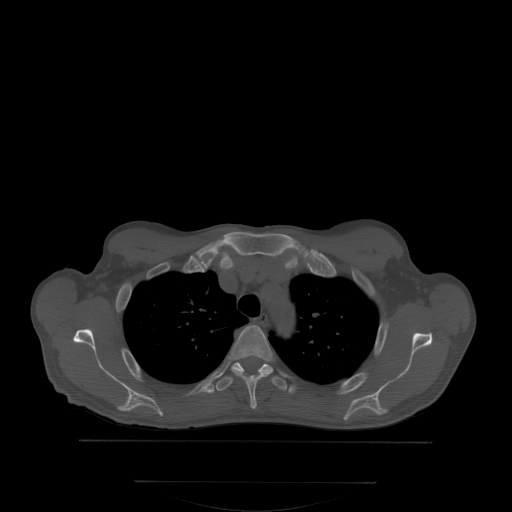
CT including the spine, one axial slice; slice 264 of 350 in the series (ordered by position); bone window (W 1800 / L 400 HU); 512 × 512 image matrix, field of view 500 × 500 mm. Patient: male, 58 years. From the clinical record (not read from this slice): primary cancer: prostate.
Structures marked on this image (semi-automatic segmentation, software-assisted and operator-edited):
- T3 vertebra: bounding box <232,325,272,408> (left, top, right, bottom; pixels)
- T4 vertebra: <216,362,285,390>